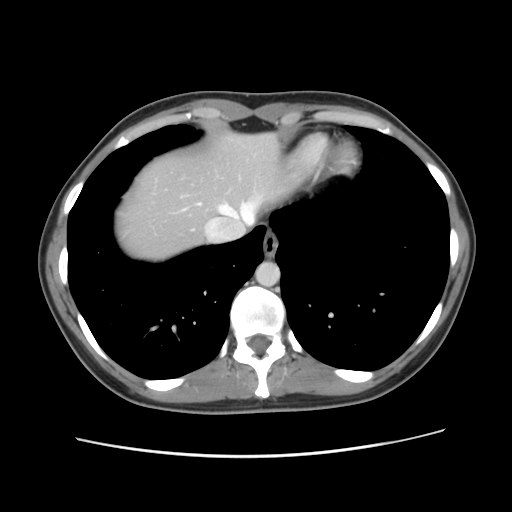
Contrast-enhanced abdominal CT, one axial slice. Slice 111 of 134 in the series (ordered by position). 120 kVp. Intravenous contrast given. Soft-tissue window (W 400 / L 40 HU). 512 × 512 image matrix, field of view 339 × 339 mm. Female patient, age 33 years. From the clinical record (not read from this slice): diagnosis: colorectal cancer liver metastases, imaged before liver resection; multiple liver metastases: yes.
Structures marked on this image (manually delineated by an expert):
- hepatic veins: bounding box (x1, y1, x2, y2) in pixels: (197, 197, 262, 224)
- liver: (115, 133, 302, 262)
- planned liver remnant (the part of the liver to remain after resection): (115, 133, 302, 261)